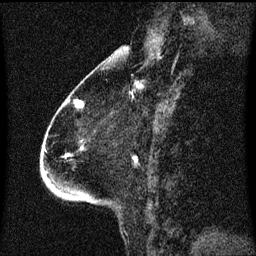
Breast MRI (dynamic contrast-enhanced), one sagittal slice. Position 27 of 60 along the scan axis. Dynamic contrast-enhanced series, image 2 of 3 at this slice position (ordered by acquisition). 1.5 T. TE 4.2 ms, TR 8.4 ms. 256 × 256 image matrix. Patient: female, 68 years. Case-level facts recorded for this patient, not image findings: setting: breast cancer imaged before/during neoadjuvant chemotherapy; receptor status: triple-negative.
Annotated regions visible in this slice (semi-automatic segmentation, software-assisted and operator-edited):
- analysis volume of interest (the breast-tissue region the enhancement analysis was run in; not a lesion): bounding box (x1, y1, x2, y2) in pixels: (43, 96, 105, 203)
- tumour enhancement mask (voxels above the 70 % enhancement threshold inside the analysis volume of interest): (78, 102, 84, 107)